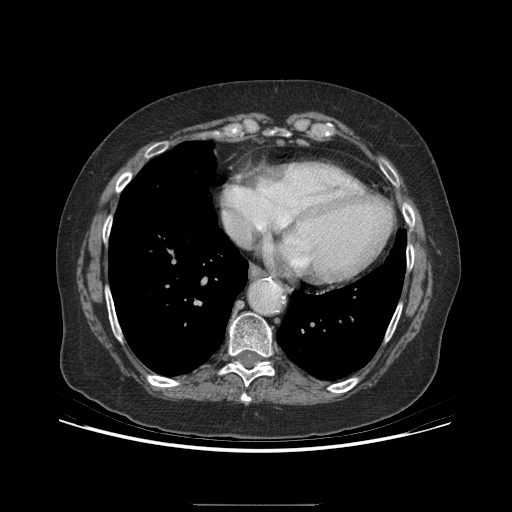
Contrast-enhanced abdominal CT (liver protocol), one axial slice; slice 190 of 192 in the series (ordered by position); reconstruction kernel STANDARD; 140 kVp; soft-tissue window (W 400 / L 40 HU); 512 × 512 image matrix, field of view 400 × 400 mm. Case-level facts recorded for this patient, not image findings: diagnosis: hepatocellular carcinoma (patient treated with transarterial chemoembolisation; whether this scan precedes or follows treatment is not stated here); TNM stage (as recorded): Stage-I; Child-Pugh class: A; tumour differentiation: moderately differentiated; tumour size: 3.2 cm.
Outlined on this slice (semi-automatic segmentation, software-assisted and operator-edited):
- abdominal aorta: bounding box <250,281,280,313> (left, top, right, bottom; pixels)